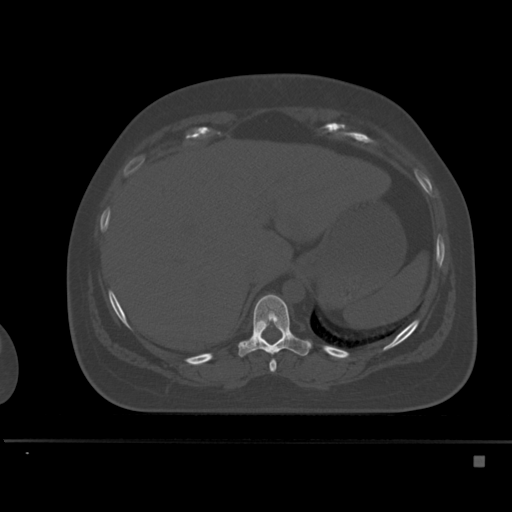
CT including the spine, one axial slice. Slice 249 of 495 in the series (ordered by position). Bone window (W 1800 / L 400 HU). 512 × 512 image matrix, field of view 404 × 404 mm. Female patient, age 33 years. From the clinical record (not read from this slice): primary cancer: breast; vertebrae with lytic lesions (as recorded): T1.
Structures marked on this image (semi-automatically segmented with operator editing):
- T10 vertebra: bounding box <238,294,311,357> (left, top, right, bottom; pixels)
- T9 vertebra: <269,359,277,372>